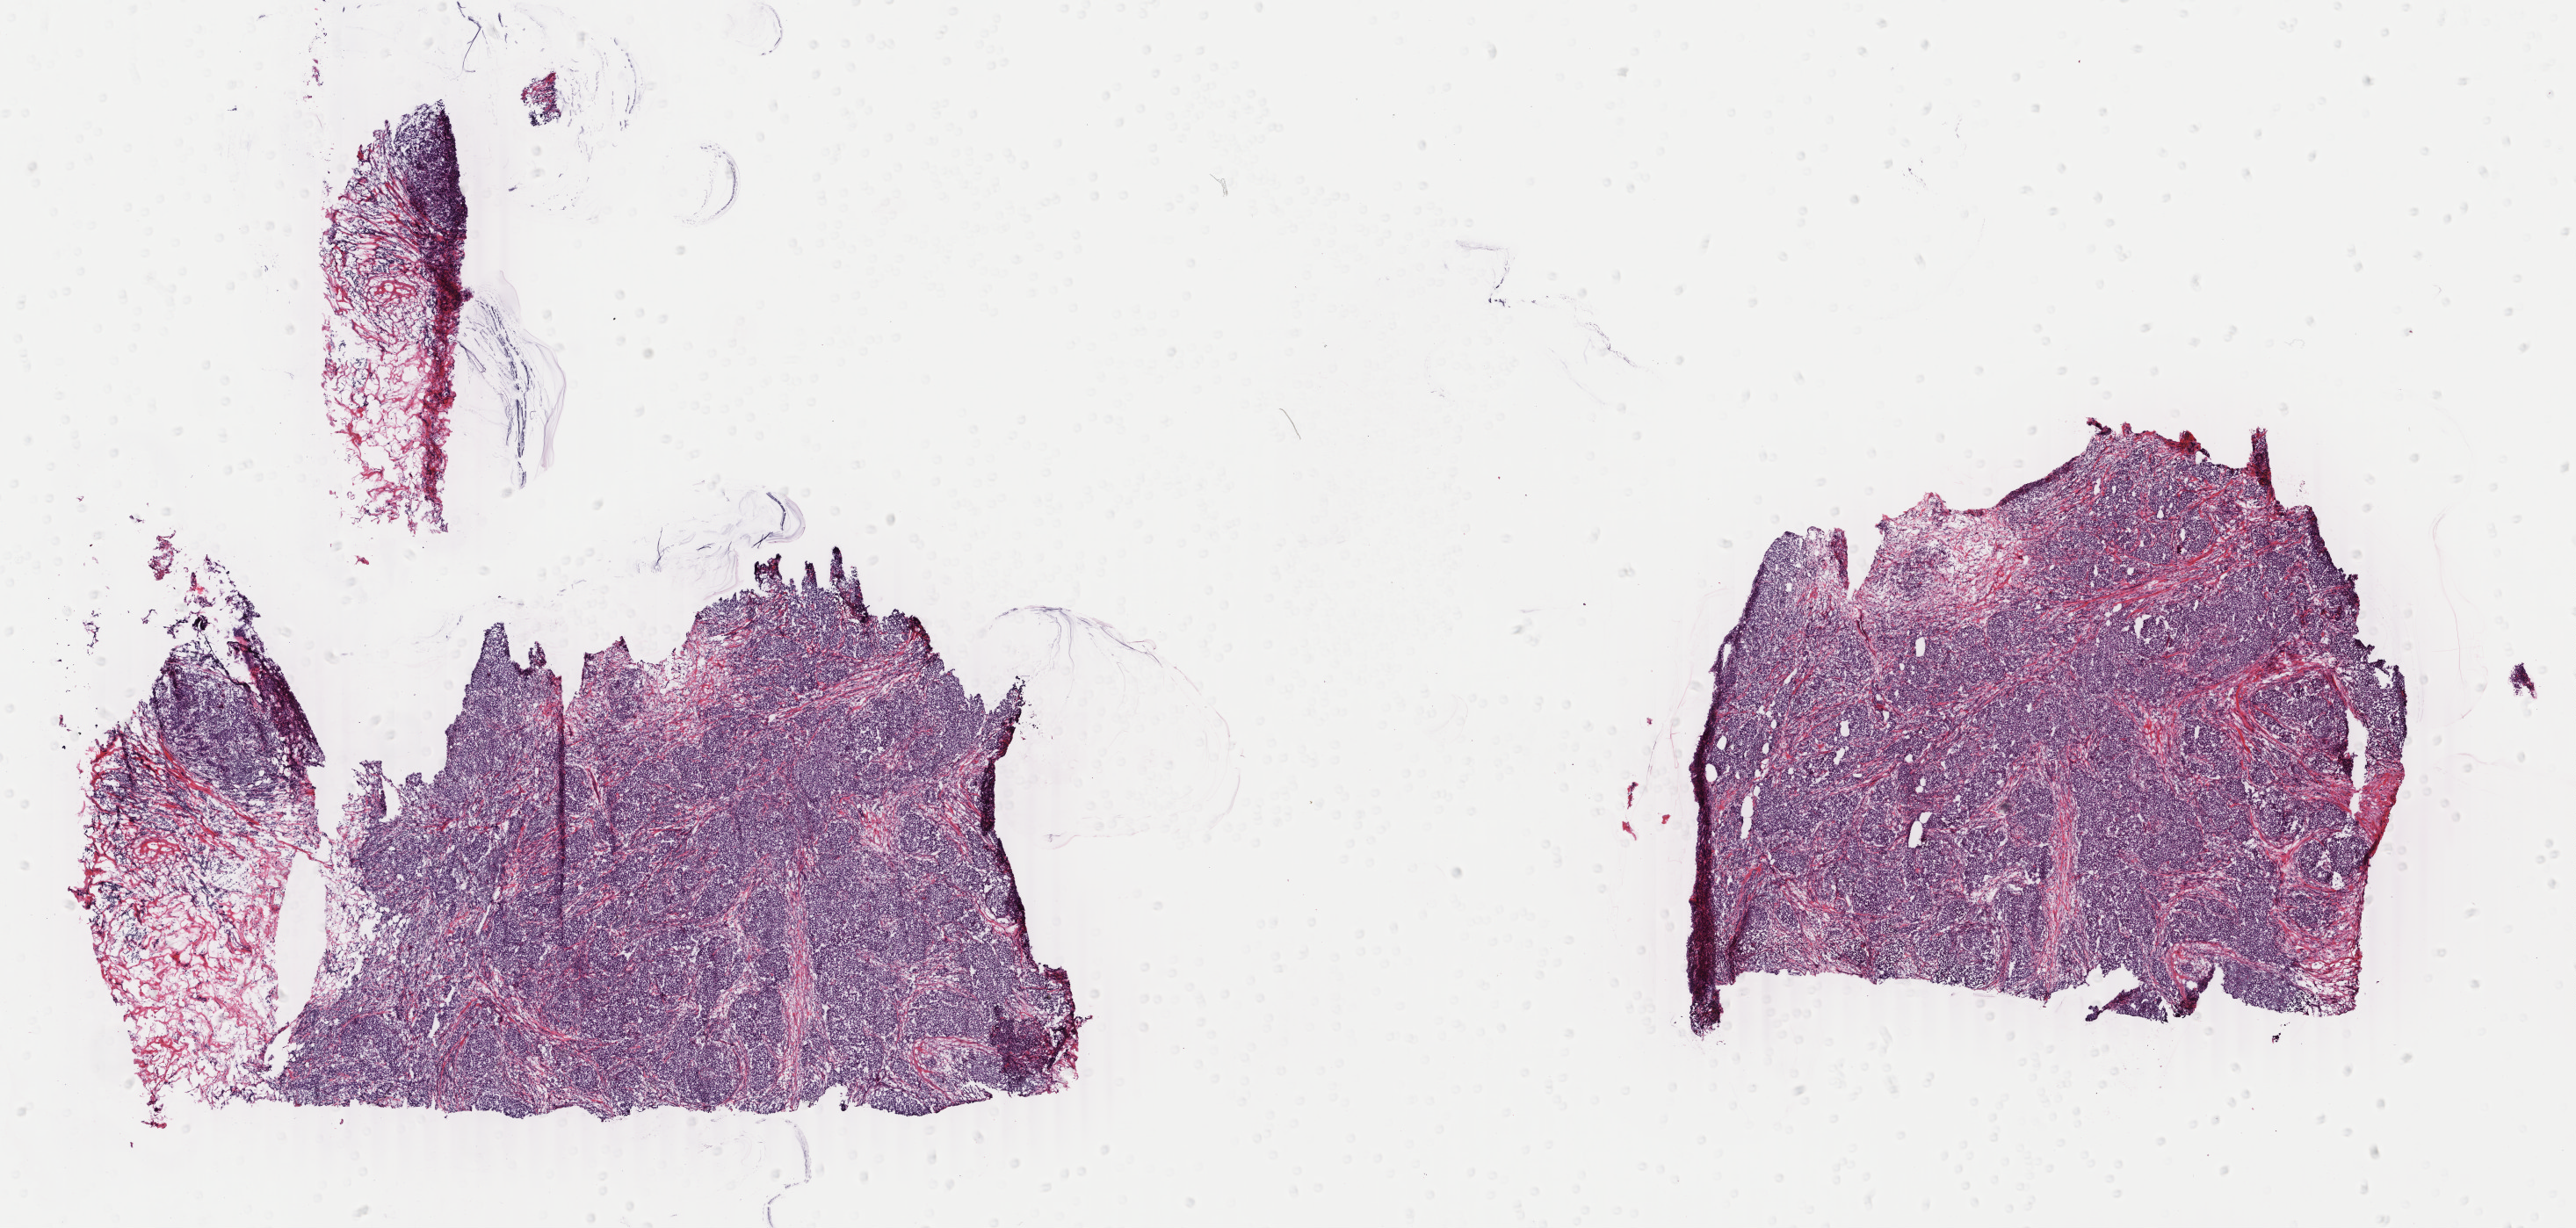
Hematoxylin and eosin (H&E) stained whole-slide image — shown as a low-resolution overview of the whole scanned area (about 23.3 x 11.1 mm, slide scanned at 40x), frozen section from the bottom of the tissue portion, breast, primary tumour sample. Female patient; age at initial diagnosis 64 years. Composition of this section per pathologist review: tumour cells 85%, tumour nuclei 90%, normal cells 0%, stromal cells 15%, necrosis 0%. Inflammatory infiltration, as recorded: lymphocyte infiltration 2%, monocyte infiltration 0%, neutrophil infiltration 0%.
Histologic diagnosis: Infiltrating duct carcinoma, NOS. Lymph nodes positive (case pathology): 0 of 2 examined. AJCC pathologic stage: IIA (6th edition).